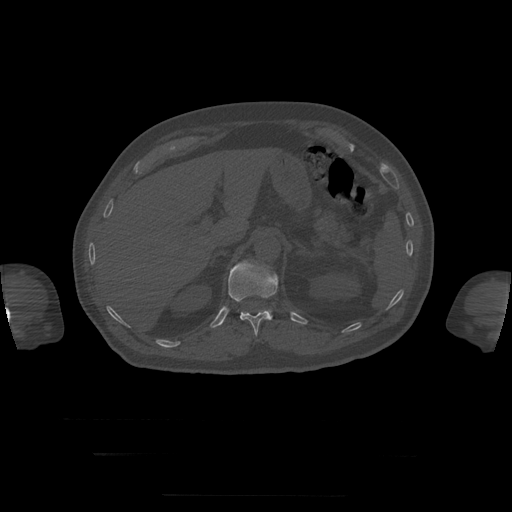
CT including the spine, one axial slice. Slice 70 of 397 in the series (ordered by position). 120 kVp. Bone window (W 1800 / L 400 HU). 1.25 mm slice thickness. 512 × 512 image matrix, field of view 510 × 510 mm. Patient age 73 years. From the clinical record (not read from this slice): primary cancer: prostate.
Annotated regions visible in this slice (semi-automatic segmentation, software-assisted and operator-edited):
- L1 vertebra: bounding box [x1, y1, x2, y2] px = [268, 310, 271, 314]
- T12 vertebra: [228, 261, 279, 336]